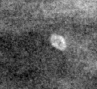
Region of interest cut from a scanned film mammogram (one marked finding); right breast; CC view.
- Marked abnormality: calcifications, morphology lucent center; BI-RADS assessment category 2; benign; no additional work-up was recommended (benign without callback).